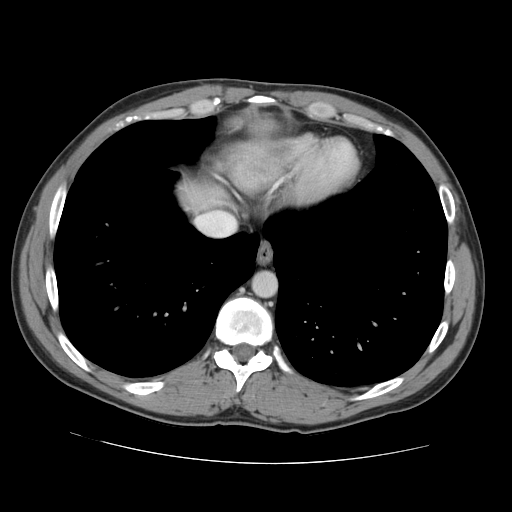
Contrast-enhanced abdominal CT, one axial slice; slice 131 of 131 in the series (ordered by position); 120 kVp; intravenous contrast given; soft-tissue window (W 400 / L 40 HU); 512 × 512 image matrix, field of view 380 × 380 mm. Male patient, age 40 years. From the clinical record (not read from this slice): diagnosis: colorectal cancer liver metastases, imaged before liver resection; multiple liver metastases: yes; largest metastasis: 2.9 cm; chemotherapy before resection: yes.
Annotated regions visible in this slice (manually delineated by an expert):
- hepatic veins: bounding box (x1, y1, x2, y2) in pixels: (202, 214, 233, 236)